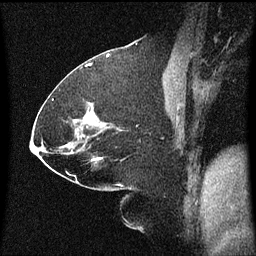
Breast MRI (dynamic contrast-enhanced), one sagittal slice. Slice 30 of 60 in the series (ordered by position). Dynamic contrast-enhanced series, image 2 of 3 at this slice position (ordered by acquisition). 1.5 T. TE 4.2 ms, TR 8 ms. 2.1 mm slice thickness. 256 × 256 image matrix, field of view 200 × 200 mm. Female patient, age 59 years.
Structures marked on this image (semi-automatic segmentation, software-assisted and operator-edited):
- analysis volume of interest (the breast-tissue region the enhancement analysis was run in; not a lesion): bounding box (x1, y1, x2, y2) in pixels: (84, 142, 103, 161)
- tumour enhancement mask (voxels above the 70 % enhancement threshold inside the analysis volume of interest): (92, 158, 99, 161)